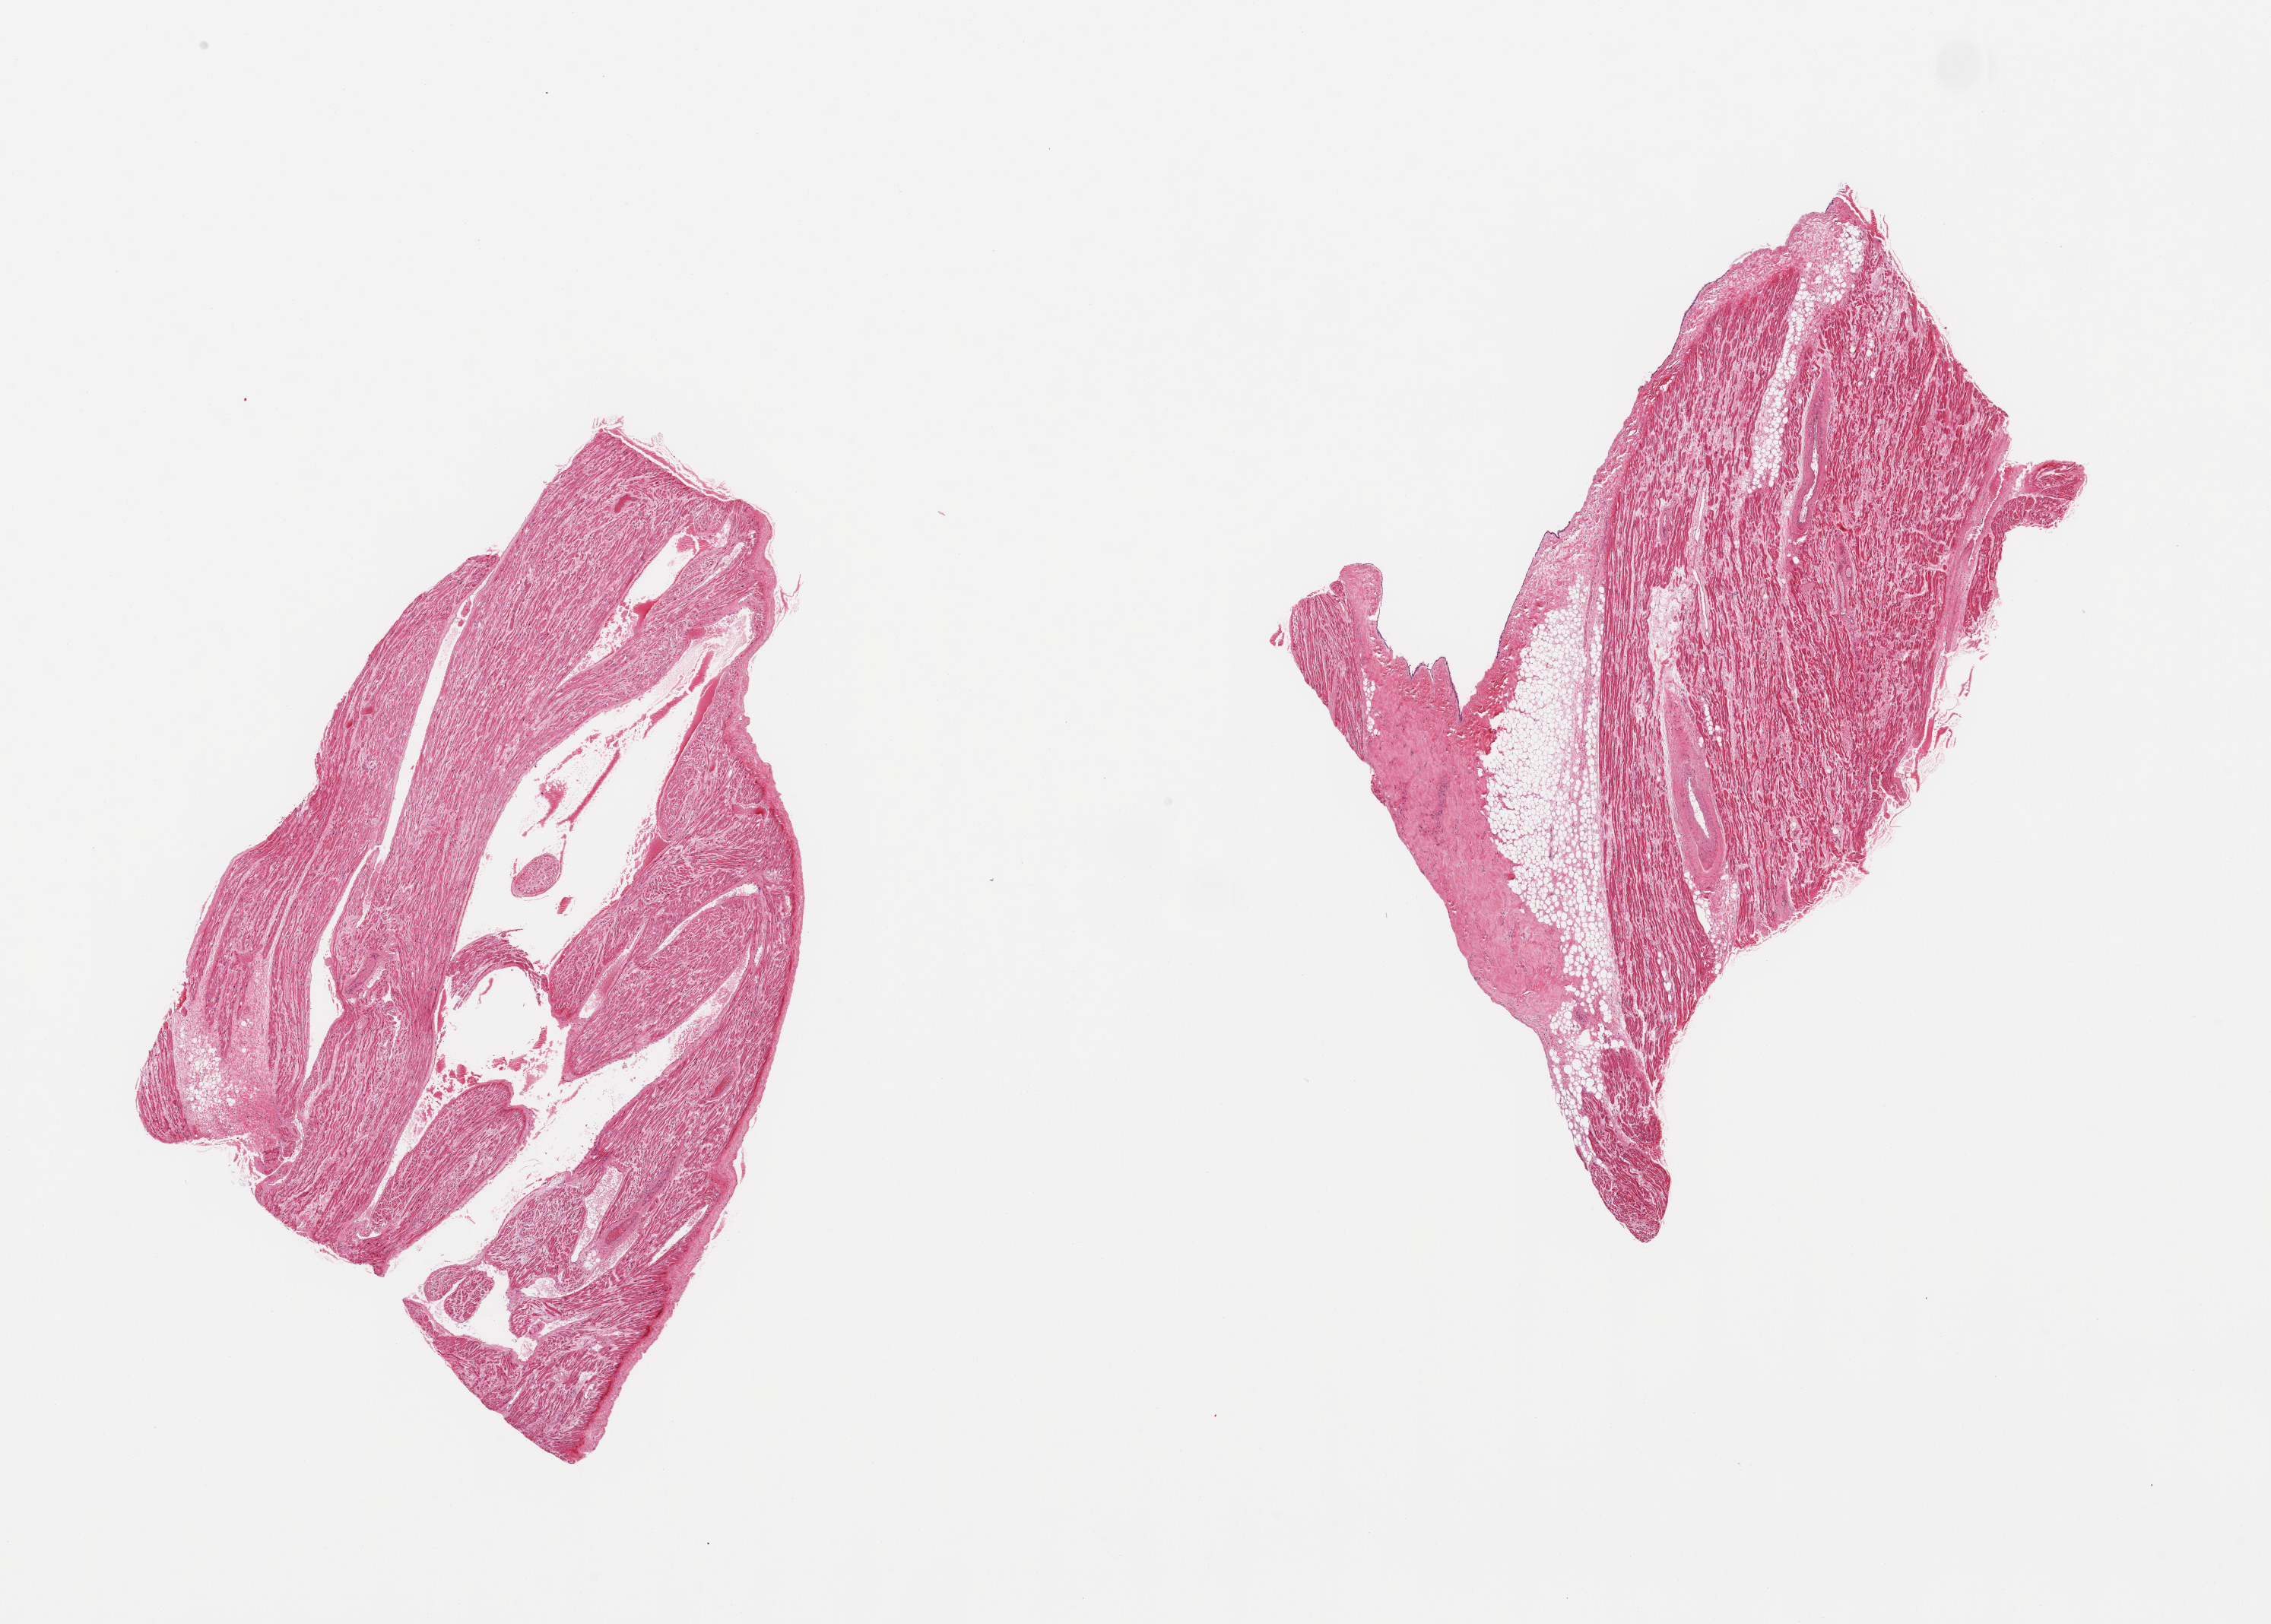
Hematoxylin and eosin (H&E) whole-slide image — a low-resolution overview of the entire scanned area, about 23.6 x 16.9 mm; PAXgene-fixed, paraffin-embedded tissue; section of auricular appendage (target tissue); donor tissue sample. Female donor.
Pathologist's review note for this sample: 2 pieces, no abnormalities.